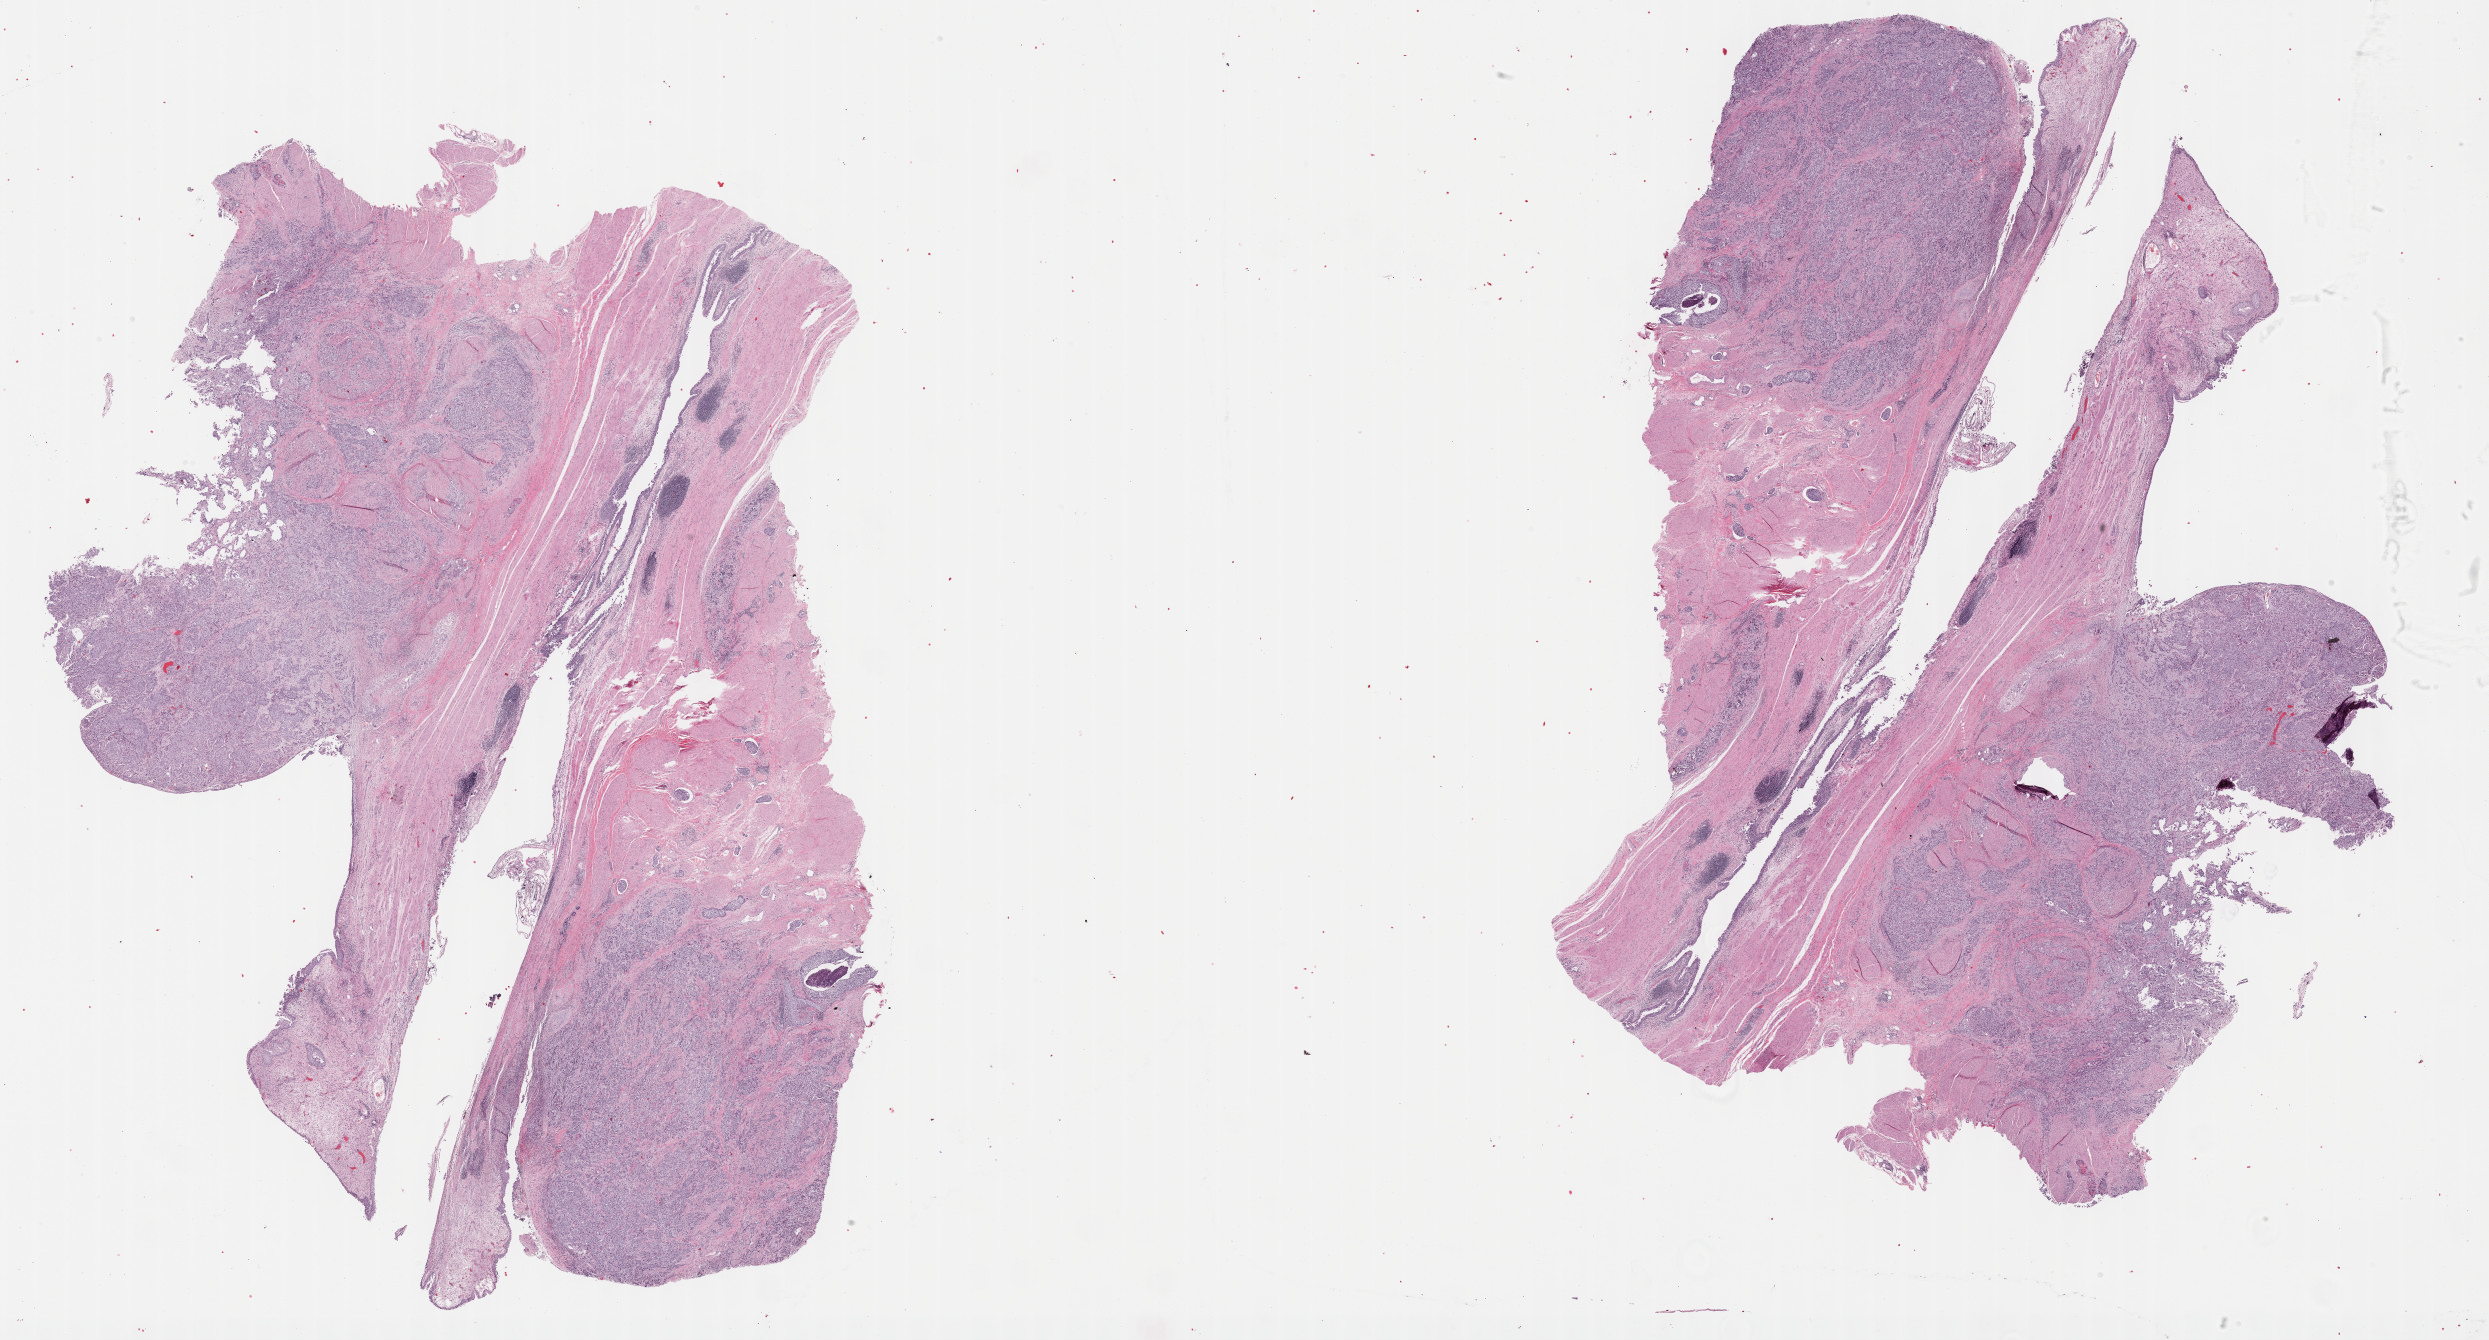
Digitized Hematoxylin and eosin (H&E) stained tissue section (whole slide), shown as a low-resolution overview of the whole scanned area (about 40.3 x 21.7 mm, slide scanned at 40x), formalin-fixed paraffin-embedded (FFPE) diagnostic section, sample: primary tumour, bladder. Male patient; age at initial diagnosis 70 years. Histologic grade: high grade.
- lymph nodes positive (case pathology): 1 of 2 examined
- AJCC pathologic stage: IV (6th edition)
- pathologic diagnosis: Transitional cell carcinoma (posterior wall of bladder)